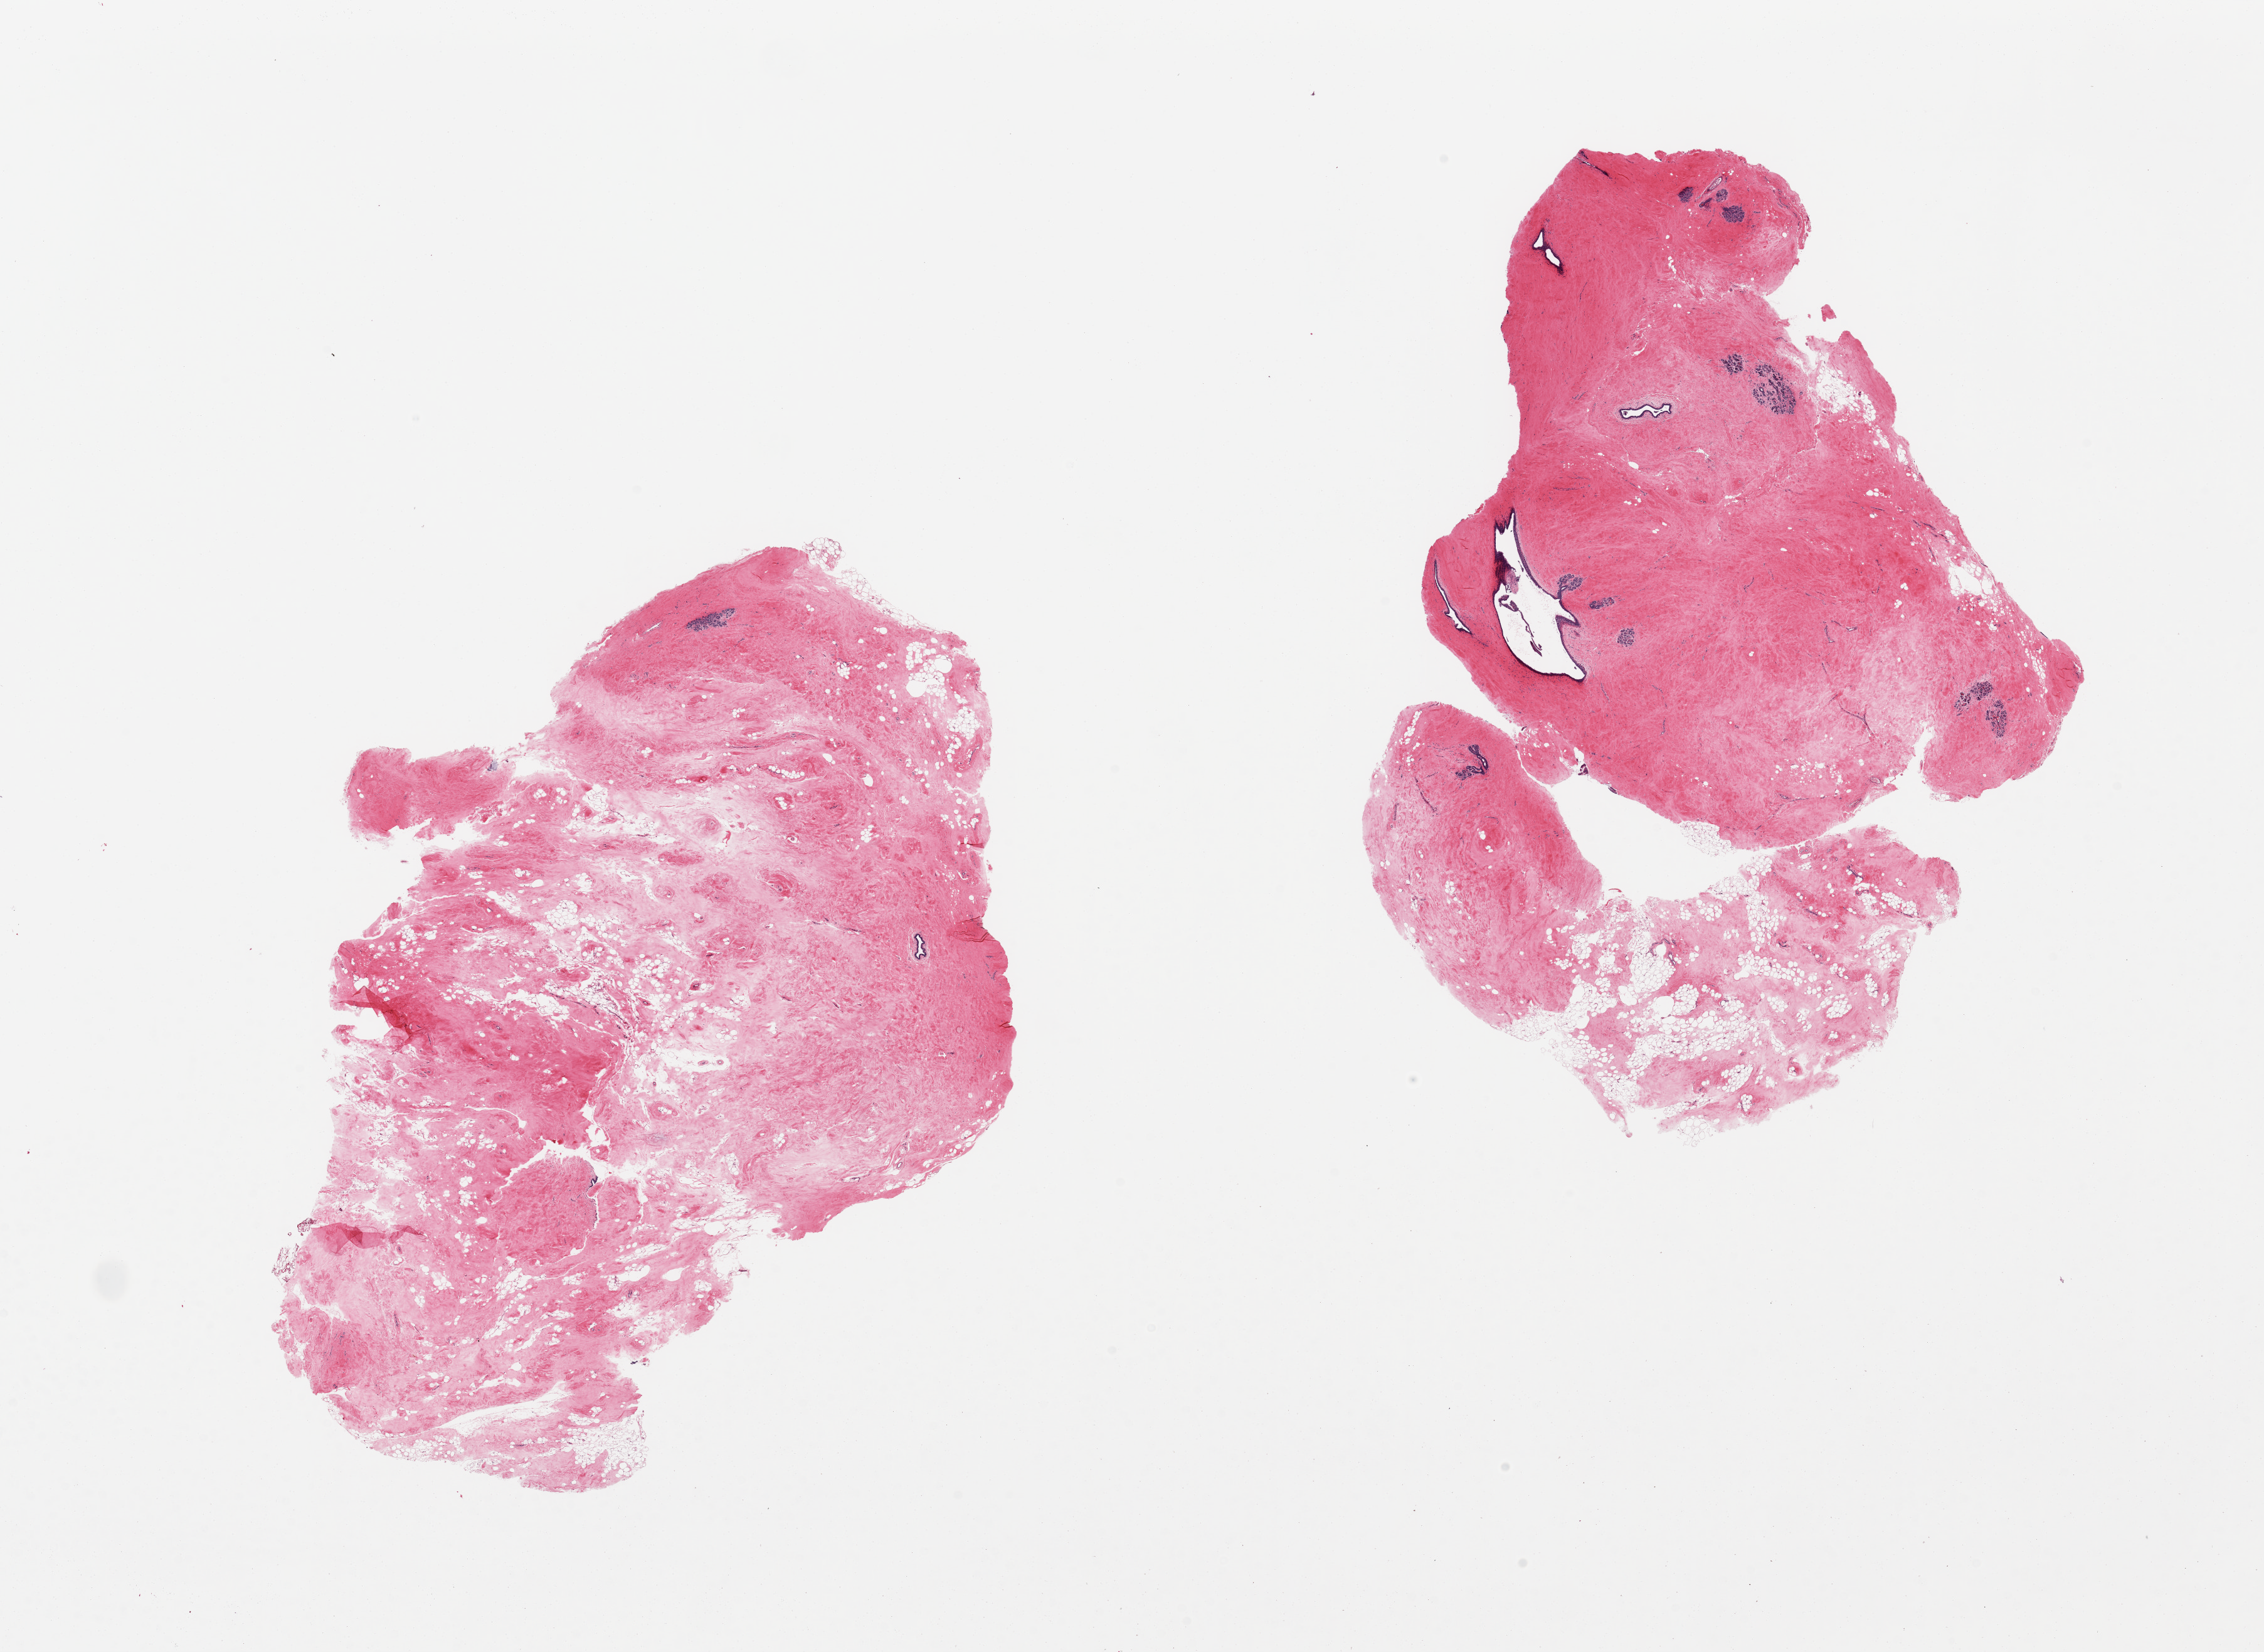
Whole-slide image, hematoxylin and eosin (H&E) stain — low-resolution overview of the scanned area, about 28.5 x 20.8 mm (acquisition: 20x scan); PAXgene-fixed, paraffin-embedded tissue; target tissue: breast; tissue donor sample. Donor sex: female.
- reviewer comment on this tissue sample: 2 pieces, fibrocystic changes, fibrous mastopathy